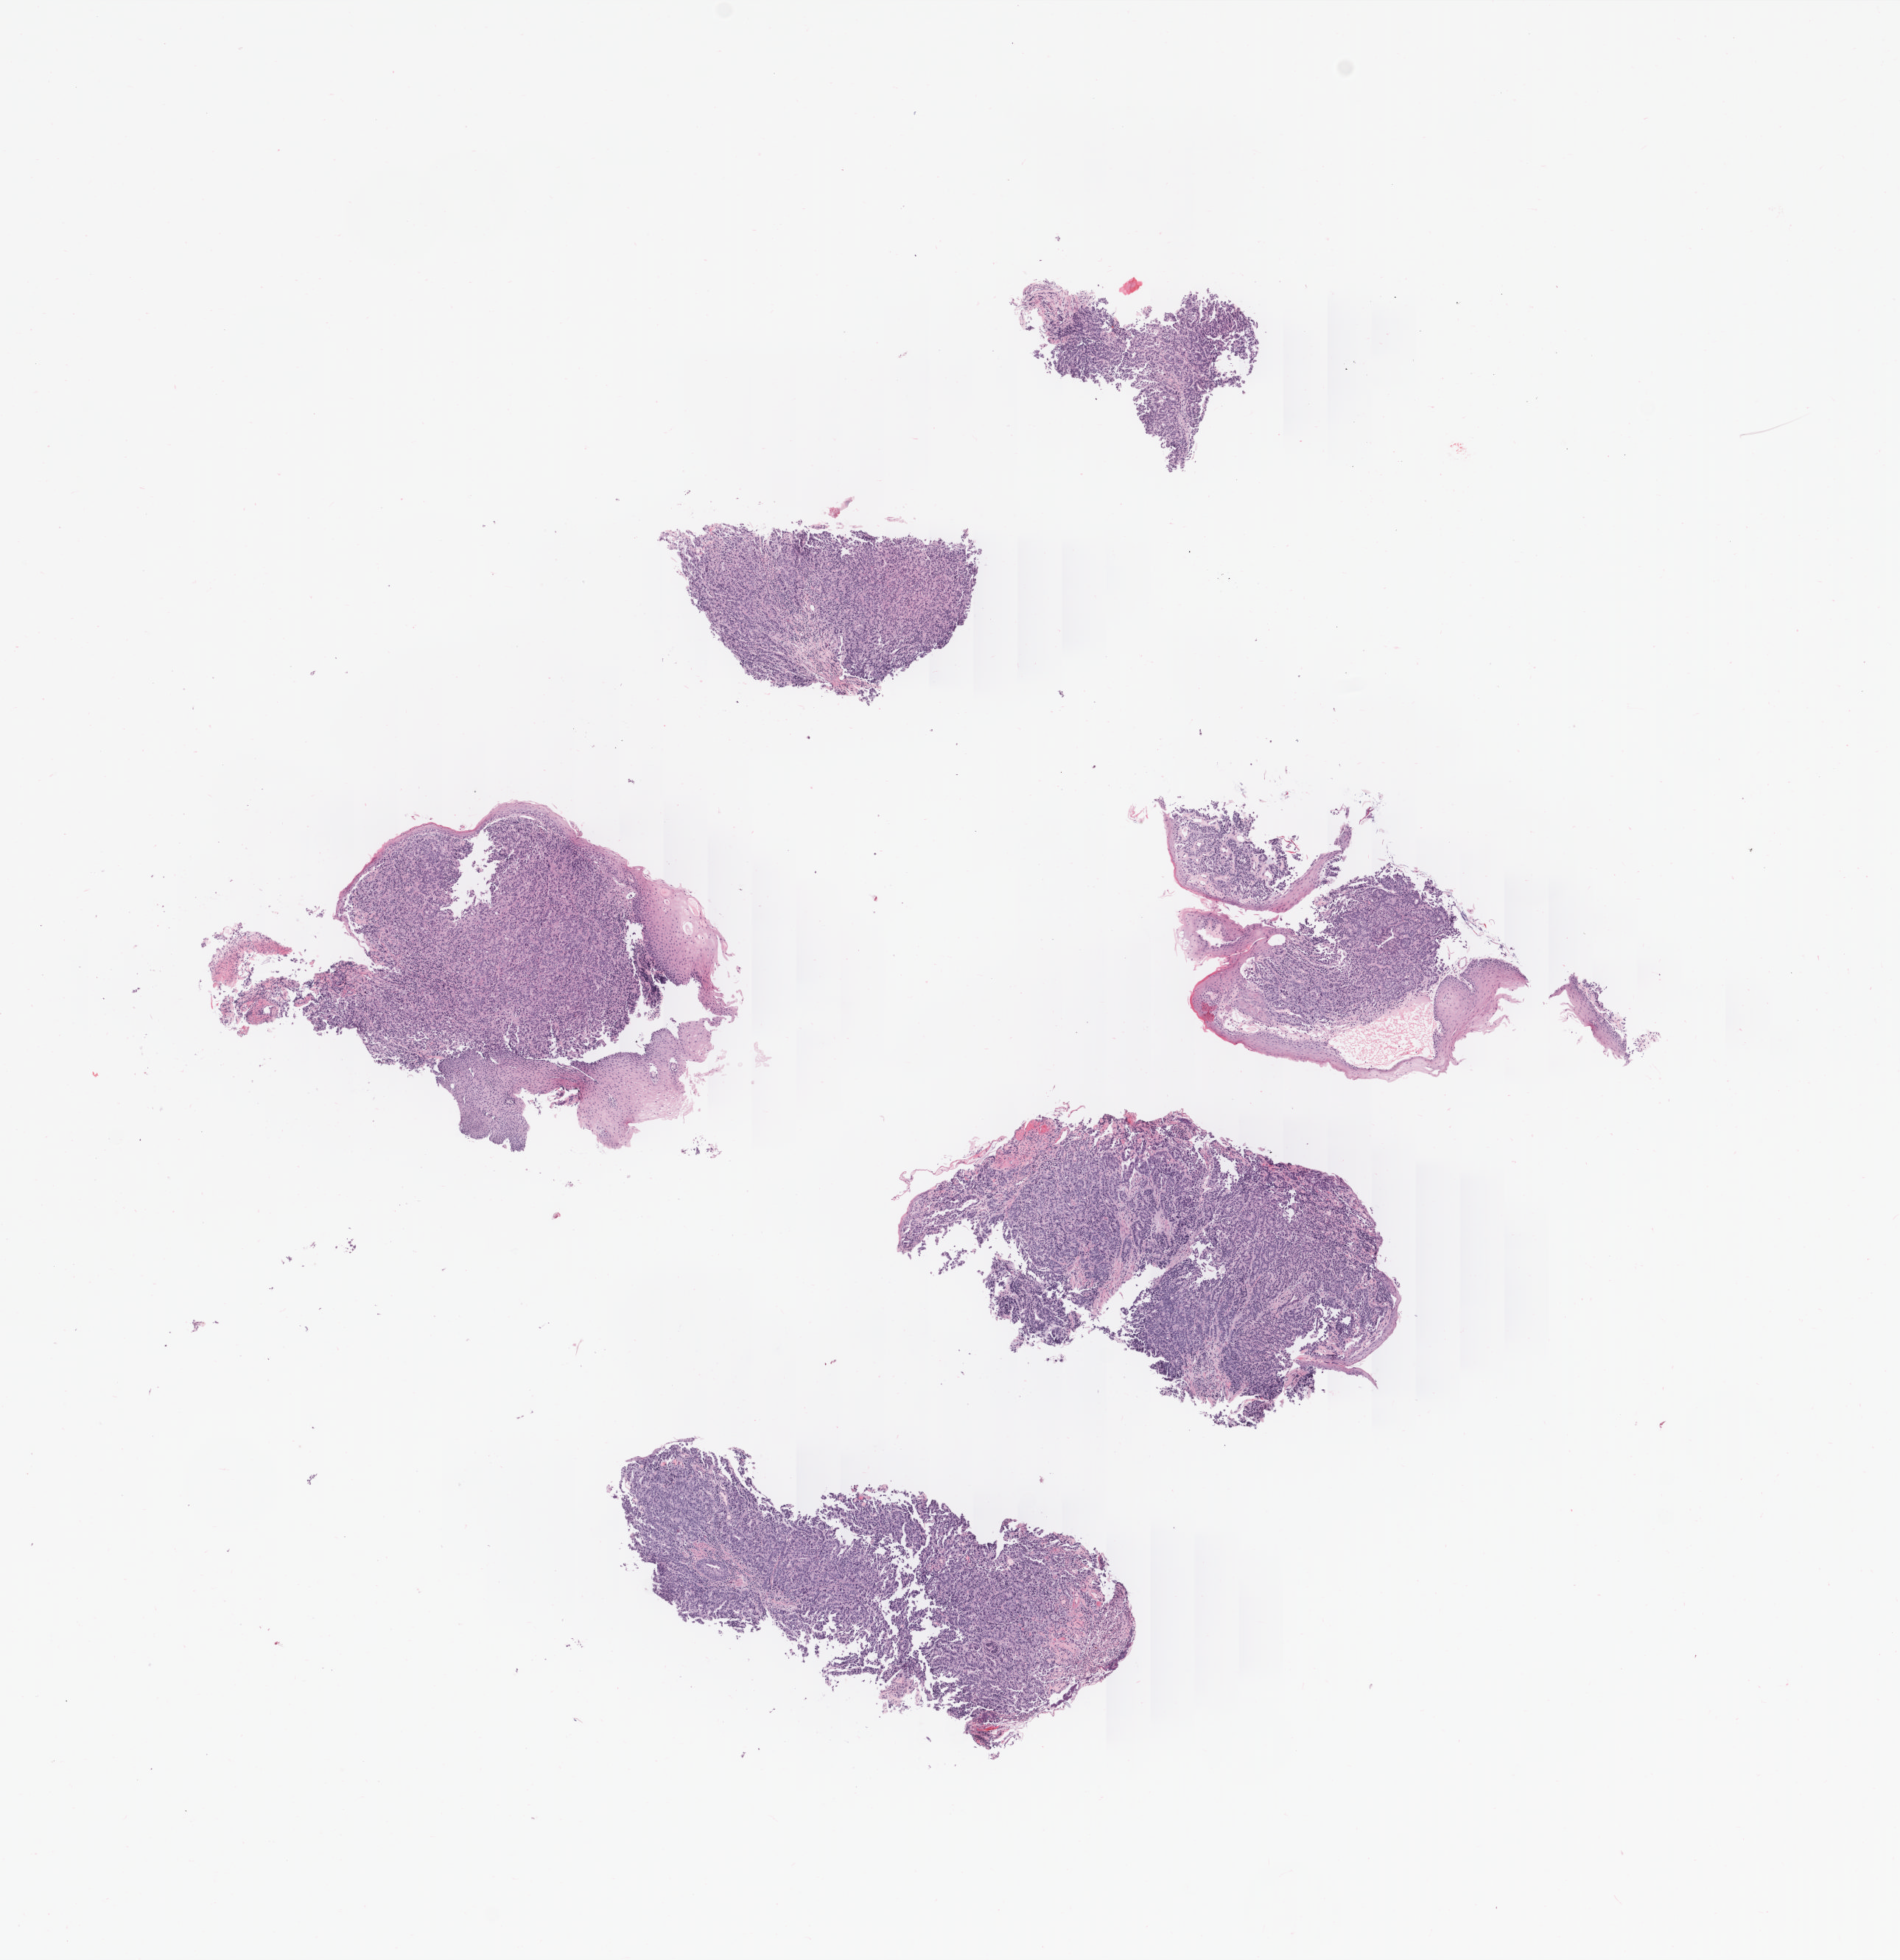
Digitized H&E tissue section (whole slide) — a low-resolution overview of the entire scanned area, about 10.4 x 10.7 mm; FFPE section; sample: primary tumour, esophagus. Male patient; age at initial diagnosis 59 years. Histologic grade: GX (grade cannot be assessed).
Pathologic diagnosis: Adenocarcinoma, NOS (lower third of esophagus). Lymph nodes positive (case pathology): 1 of 1 examined.